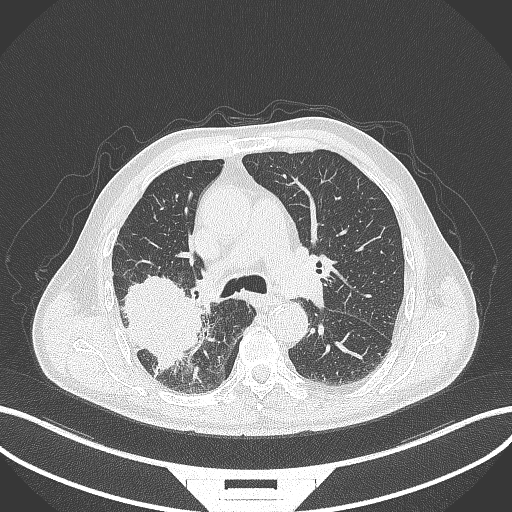
Chest CT, one axial slice. Position 257 of 429 along the scan axis. 120 kVp. Lung window (W 1500 / L -600 HU). 1 mm slice thickness. 512 × 512 image matrix, field of view 400 × 400 mm. Patient: male, 72 years. From the clinical record (not read from this slice): clinical TNM (as recorded): T3 N2 M0.
Annotated regions visible in this slice (rectangle marked by the reading radiologist):
- lung tumour (recorded histology: adenocarcinoma): bounding box [x1, y1, x2, y2] px = [117, 271, 206, 373]